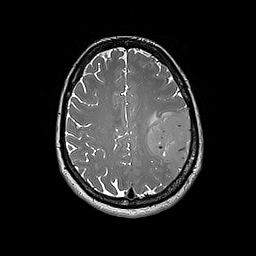
Brain MRI from a brain-tumour surgery series, one axial slice. Position 70 of 192 along the scan axis. 1 mm slice thickness. 256 × 256 image matrix. From the clinical record (not read from this slice): histopathology: Glioblastoma; WHO grade: 4; IDH mutation: no.
Structures marked on this image (outlined manually by an expert reader):
- tumour: bounding box (x1, y1, x2, y2) in pixels: (147, 114, 192, 166)